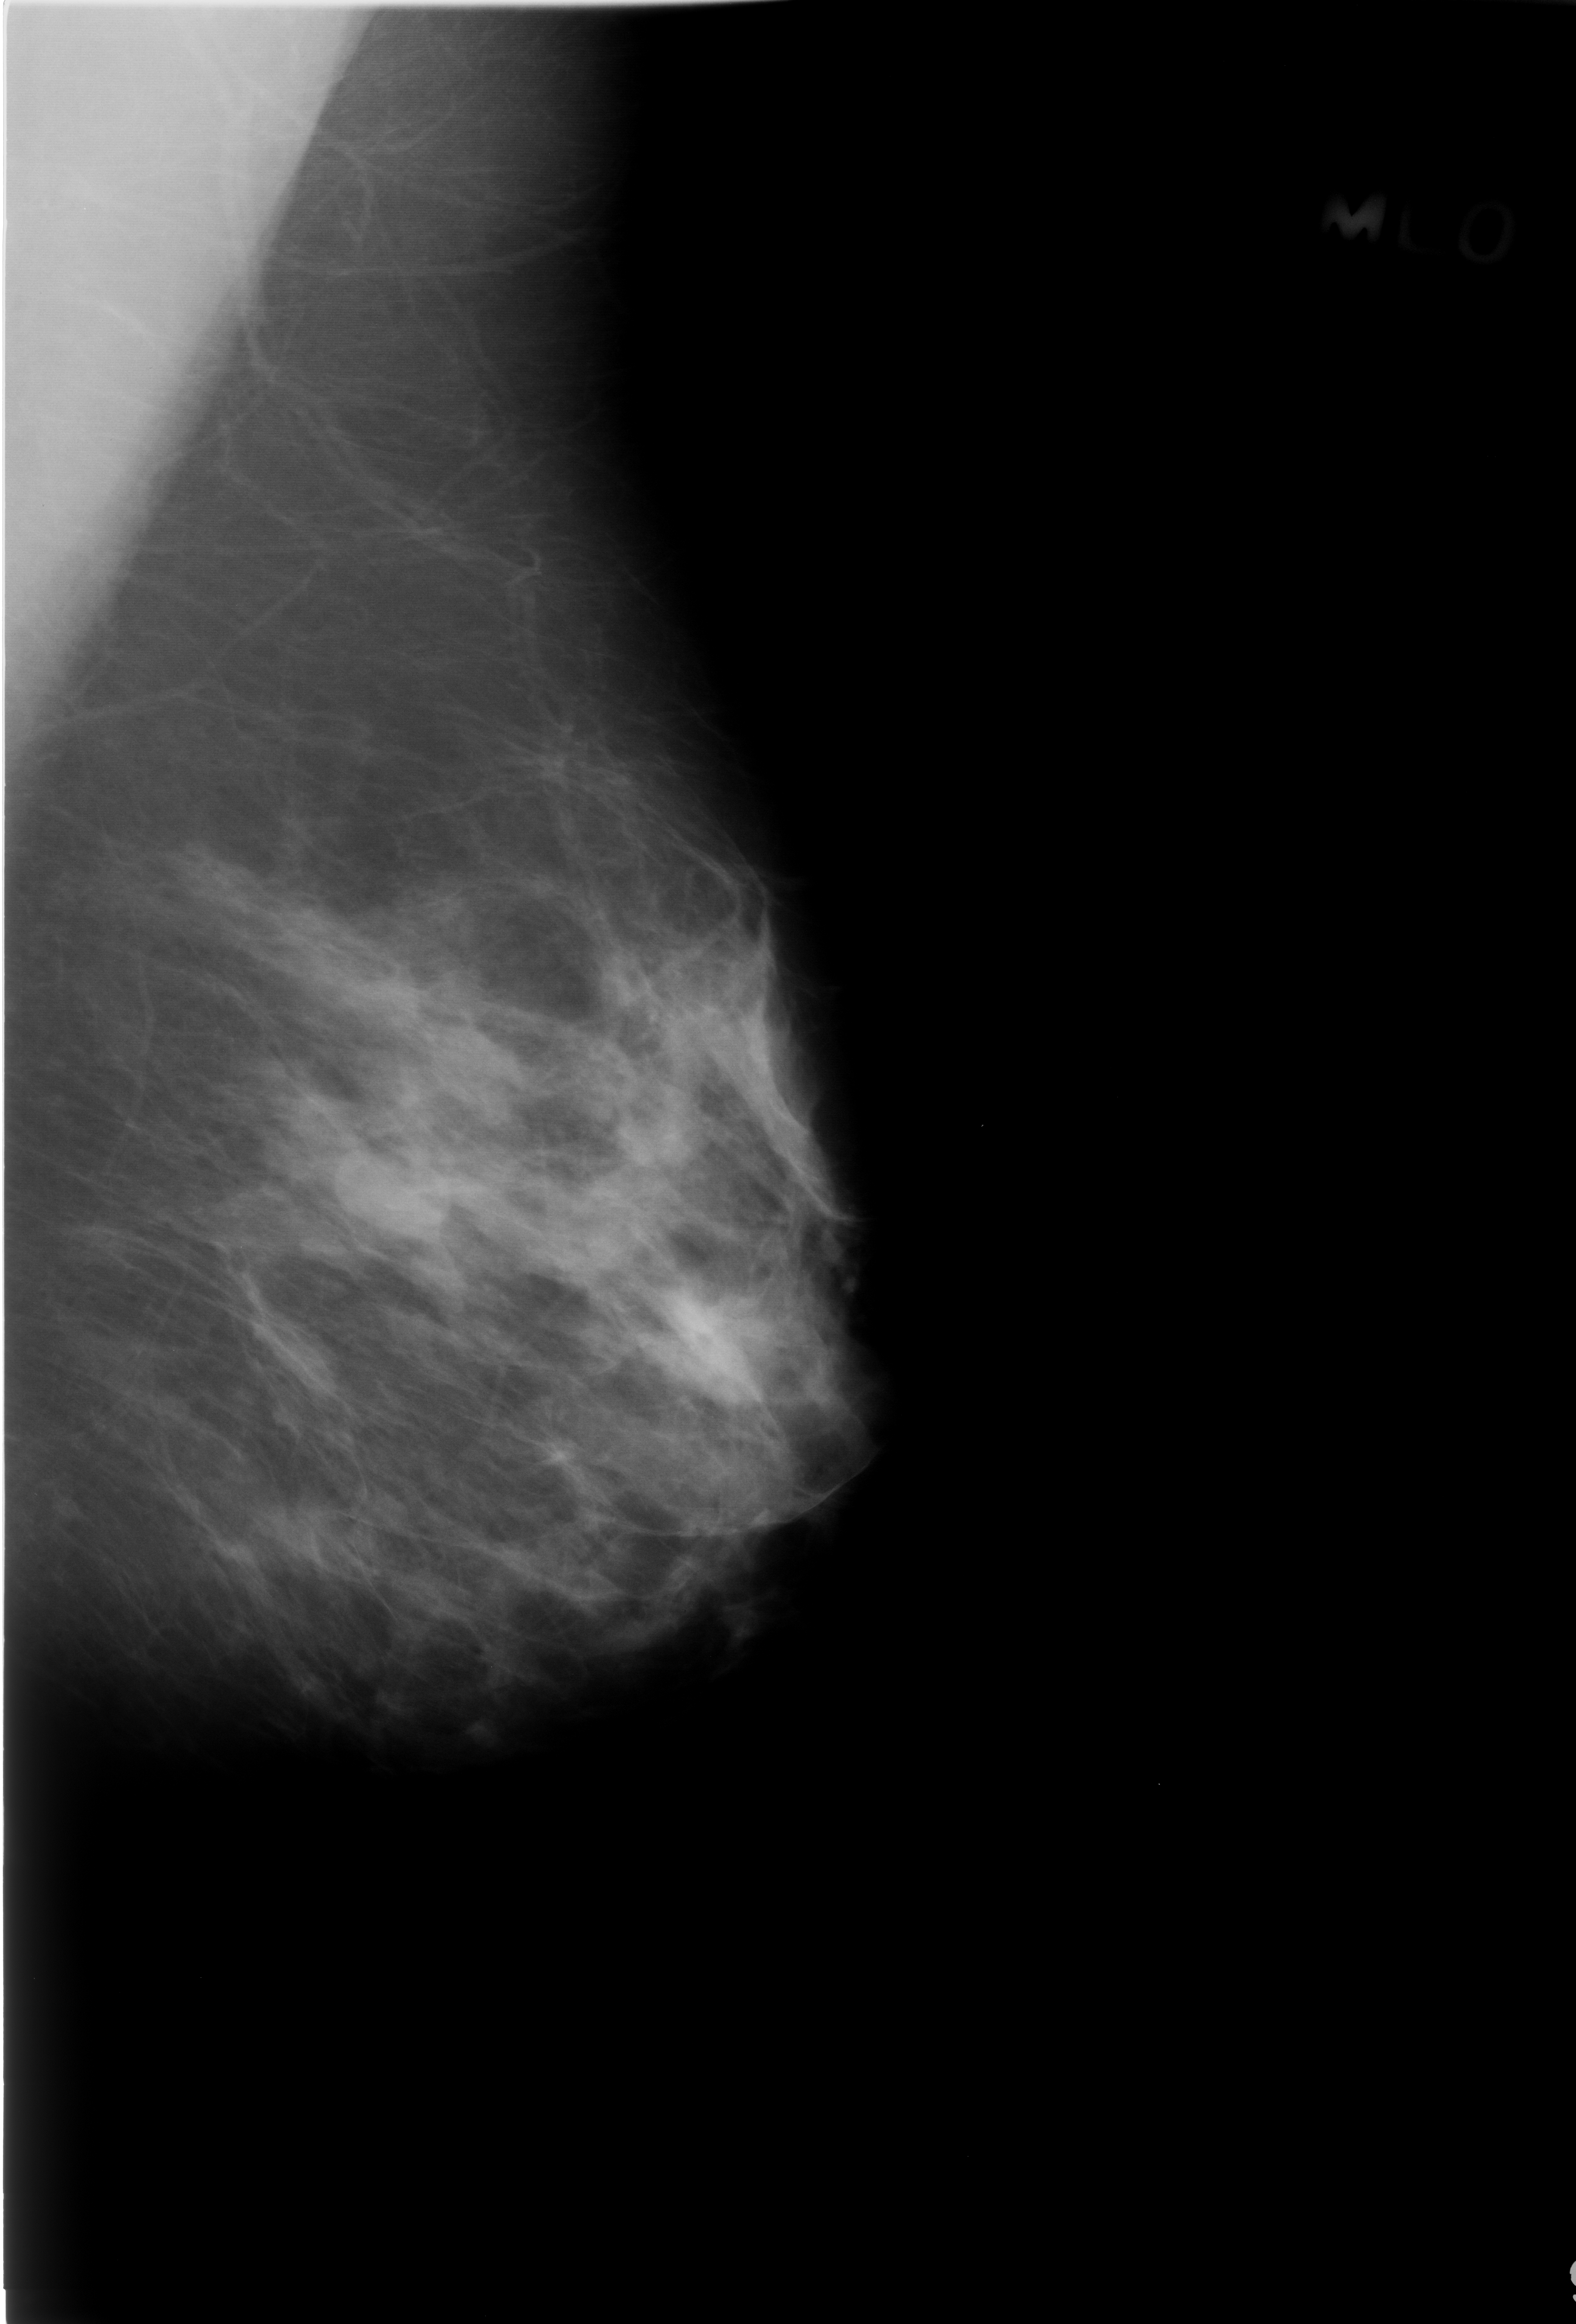
Digitized screen-film mammogram. Left breast. MLO view. BI-RADS breast density category 2 (scale 1–4). 1576 × 2324 image matrix.
Marked abnormalities (boxes around the expert regions of interest):
- mass, shape oval, margins circumscribed; BI-RADS assessment category 3; subtlety rating 4 on a 1 (subtle) to 5 (obvious) scale; pathology result (as recorded, not read from the image): benign: bounding box [x1, y1, x2, y2] px = [328, 1140, 458, 1245]